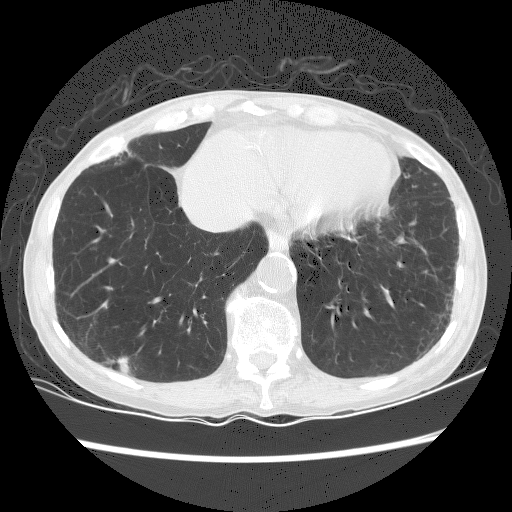
Chest CT (low-dose screening protocol), one axial image, baseline annual screen, lung window (W 1500 / L -600 HU), 2.5 mm slice thickness, lung (sharp) reconstruction kernel (BONE), slice 102 of 156 in the series. Female participant, aged 70 years at enrolment.
- Expert reader's lesion annotation, box from (x=98, y=344) to (x=151, y=385) px.
- The screening reader recorded 2 non-calcified nodules or masses ≥4 mm on this exam; which of them this box marks is not recorded.
- Lung cancer was diagnosed 125 days after this screen: squamous cell carcinoma, NOS, right lower lobe, well differentiated (G1), stage IA (AJCC 6th edition), 25 mm at pathology.